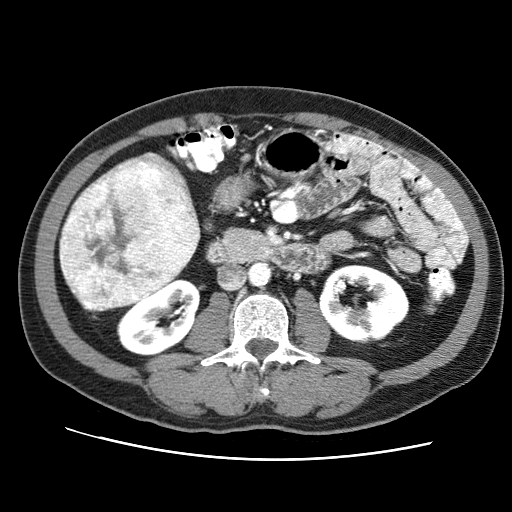
Contrast-enhanced abdominal CT (liver protocol), one axial slice. Position 21 of 71 along the scan axis. Soft-tissue window (W 400 / L 40 HU). 2.5 mm slice thickness. 512 × 512 image matrix, field of view 360 × 360 mm. Case-level facts recorded for this patient, not image findings: diagnosis: hepatocellular carcinoma (patient treated with transarterial chemoembolisation; whether this scan precedes or follows treatment is not stated here); TNM stage (as recorded): Stage-II; Child-Pugh class: A; tumour differentiation: well differentiated.
Structures marked on this image (semi-automatic segmentation, software-assisted and operator-edited):
- liver parenchyma outside the tumour (the mass and vessels are separate outlines, so this box may not span the whole liver): box from (x=59, y=156) to (x=199, y=311) px
- mass: (x=58, y=151)–(x=200, y=311)